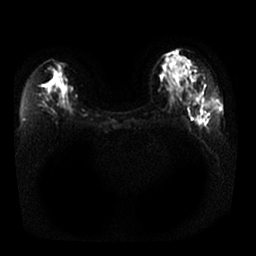
Breast MRI, one axial slice. Slice 15 of 25 in the series (ordered by position). Diffusion-weighted series; image 2 of 4 stored at this slice position (different b-values; order by instance number). 1.5 T. 4 mm slice thickness. 256 × 256 image matrix. Female patient.
Outlined on this slice (manually delineated by an expert):
- tumour on diffusion-weighted imaging: box from (x=202, y=98) to (x=204, y=102) px